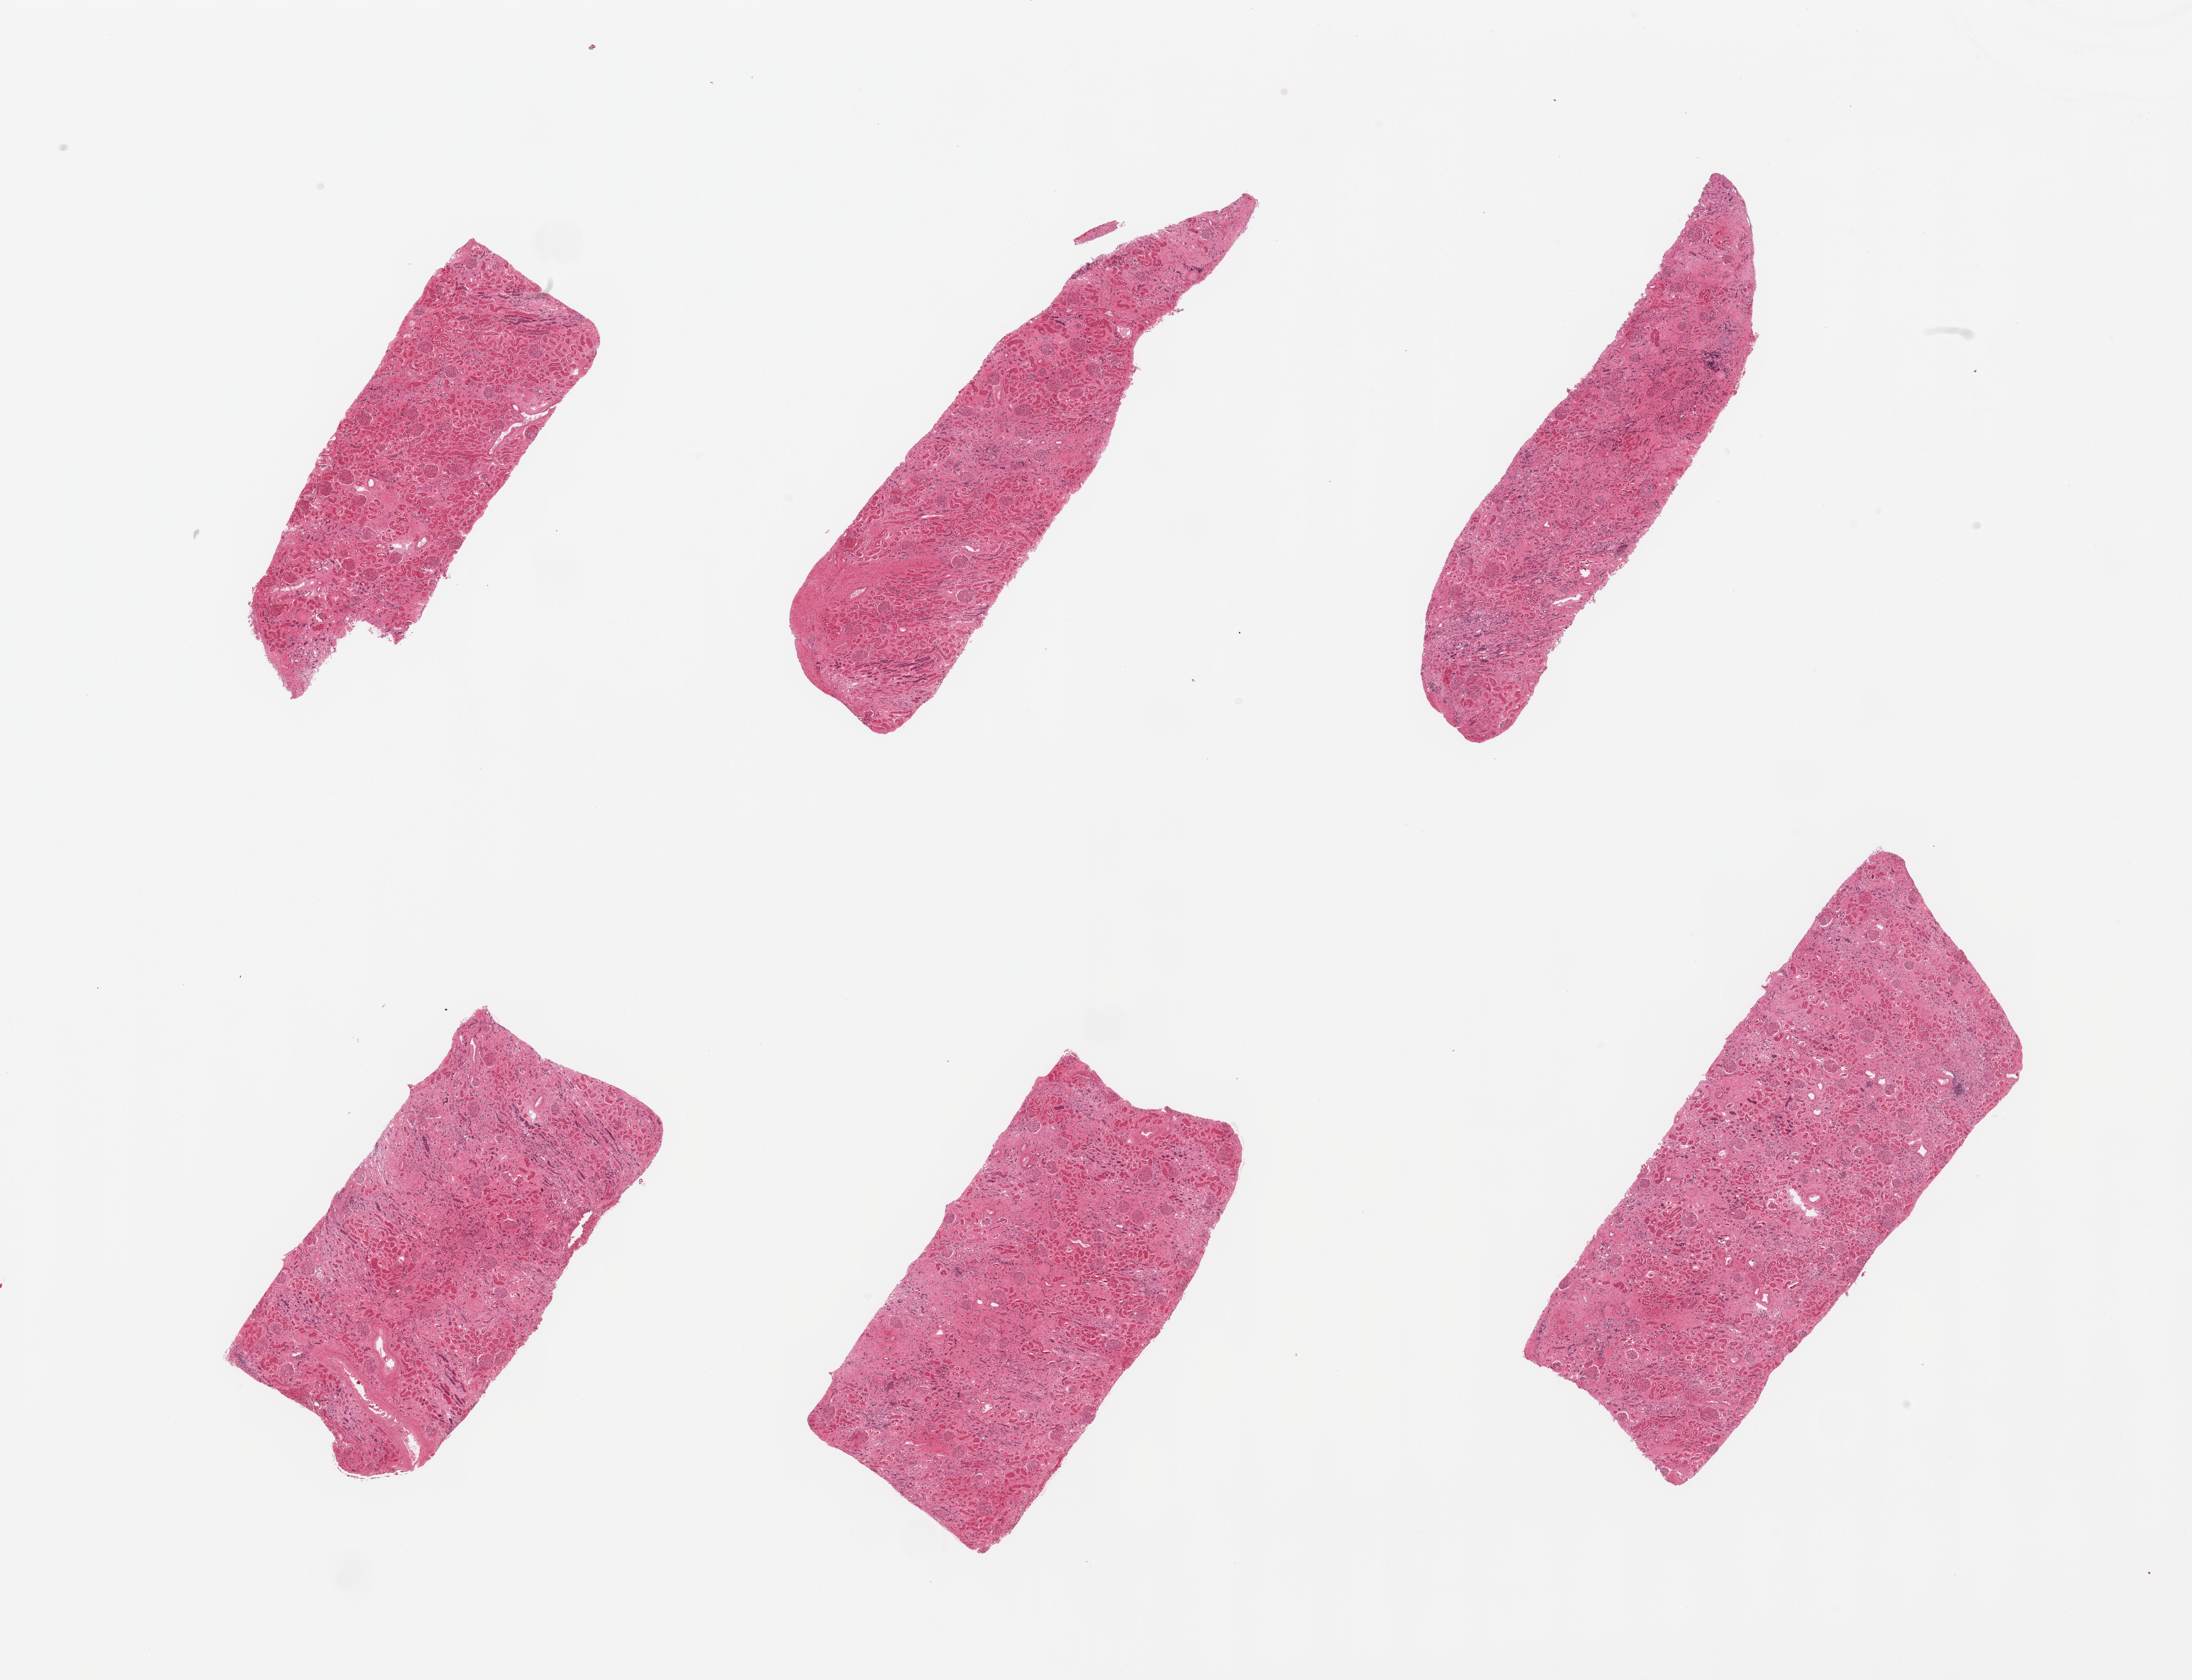
Digitized hematoxylin and eosin (H&E)-stained section, brightfield — shown as a low-resolution overview of the whole scanned area (about 27.6 x 21.1 mm), PAXgene-fixed paraffin-embedded (PFPE) section, sampled site (target tissue): renal cortex, donor tissue sample. Donor sex: male.
* reviewer comment on this tissue sample: 6 pieces; tubular atrophy and interstitial fibrosis, occasional sclerotic glomeruli, arteriosclerosis